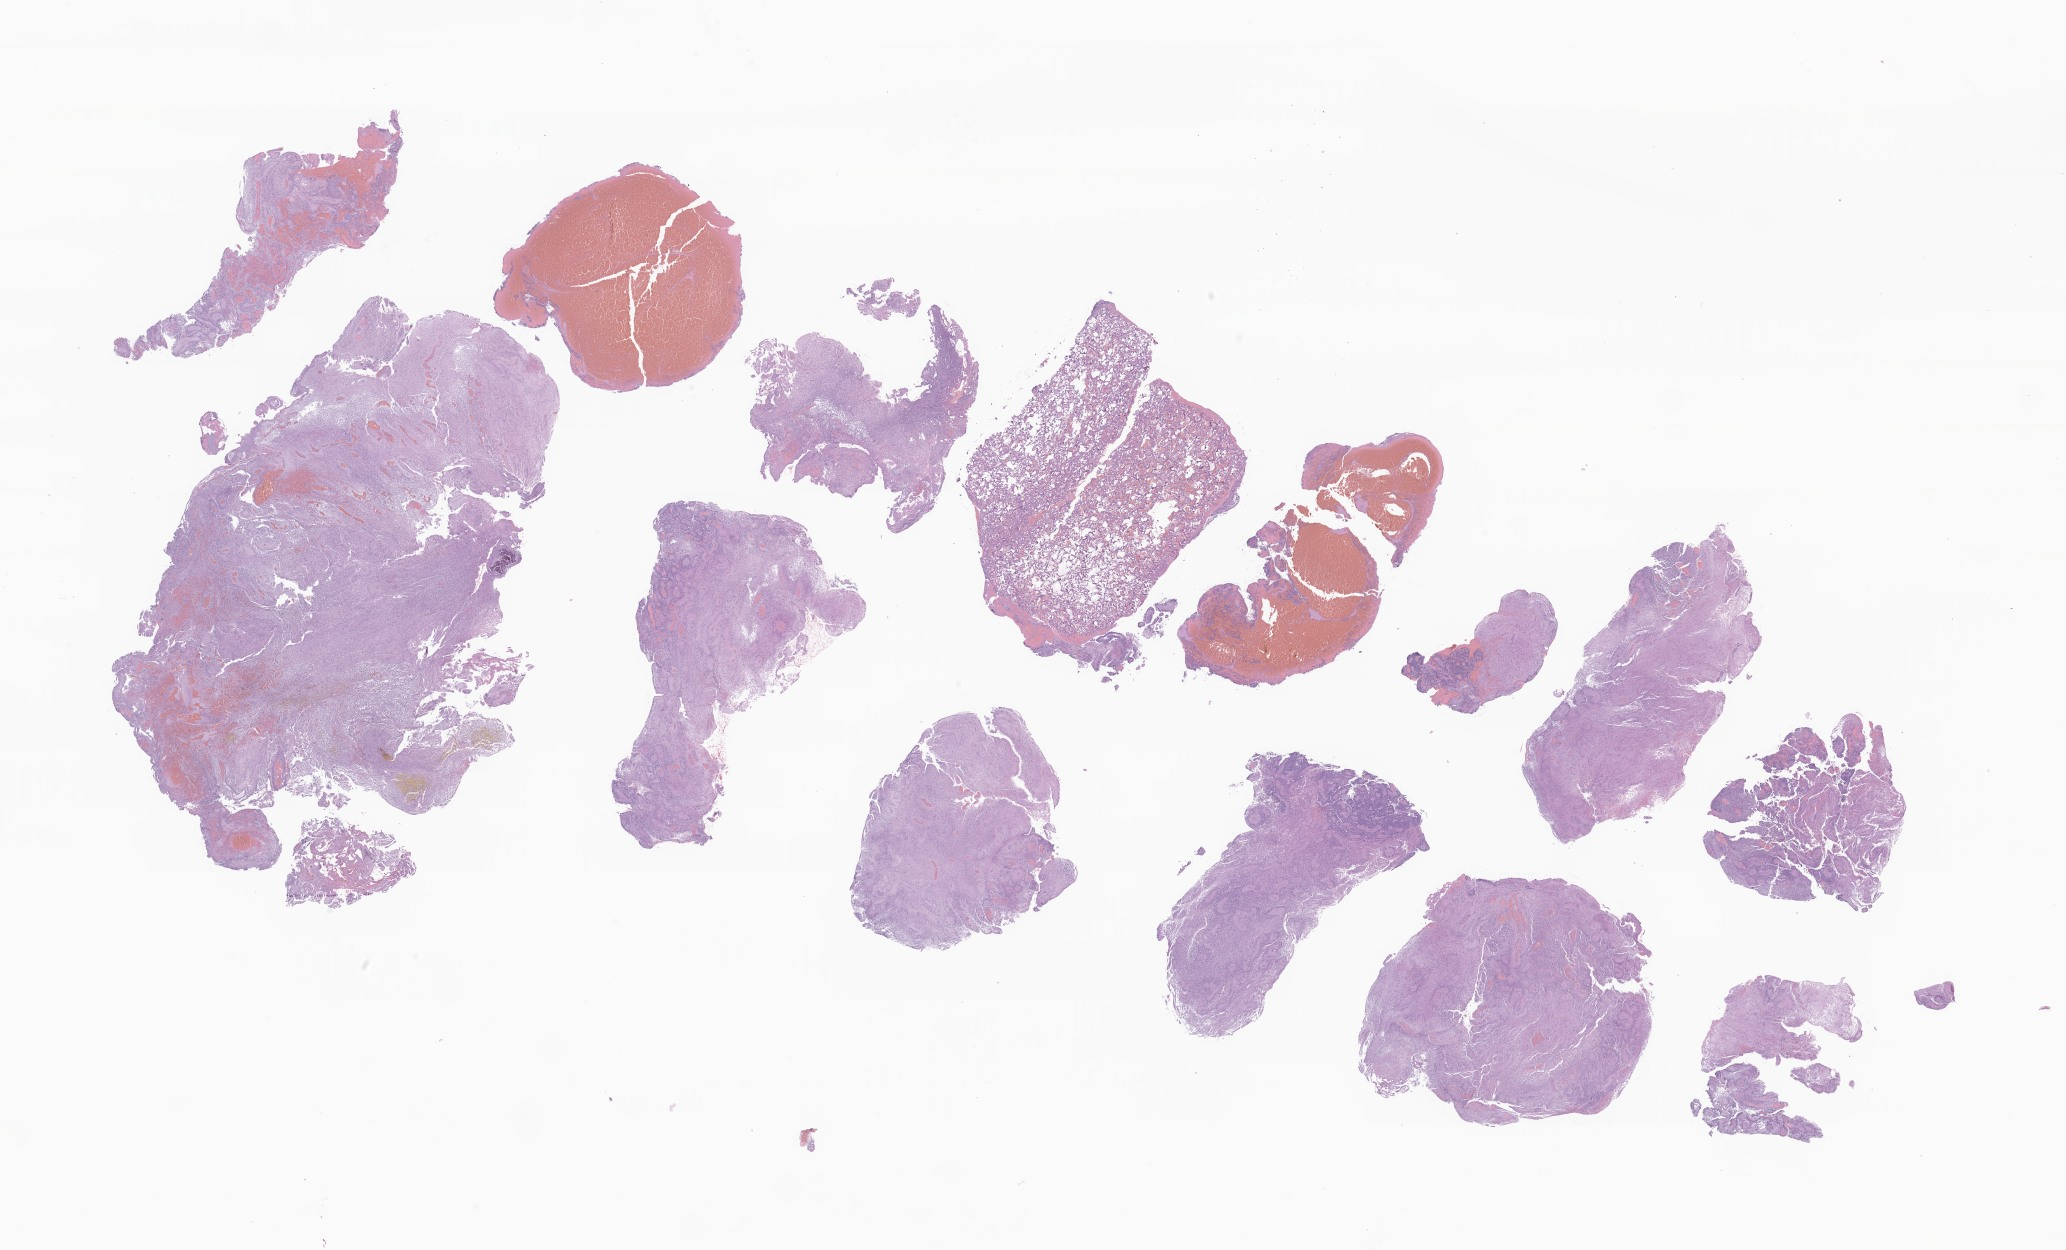
Digitized haematoxylin and eosin-stained section of tumor tissue from the brain, whole scanned area (about 34.8 x 21.1 mm) shown as a low-resolution overview, FFPE section. Patient: male, age 621 days (about 1.7 years).
* recorded diagnosis: Neoplasm, uncertain whether benign or malignant